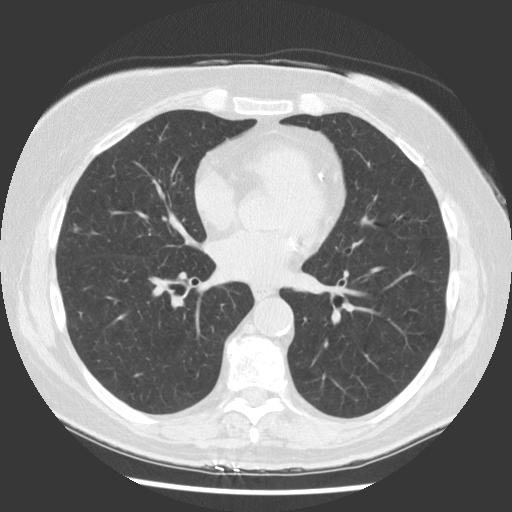
Low-dose screening chest CT, one axial slice. Position 74 of 142 along the scan axis. Lung window (W 1500 / L -600 HU). 512 × 512 image matrix.
Structures marked on this image (manually delineated by an expert):
- lesion 1 (tumor, middle lobe of right lung): bounding box <73,224,81,233> (left, top, right, bottom; pixels)